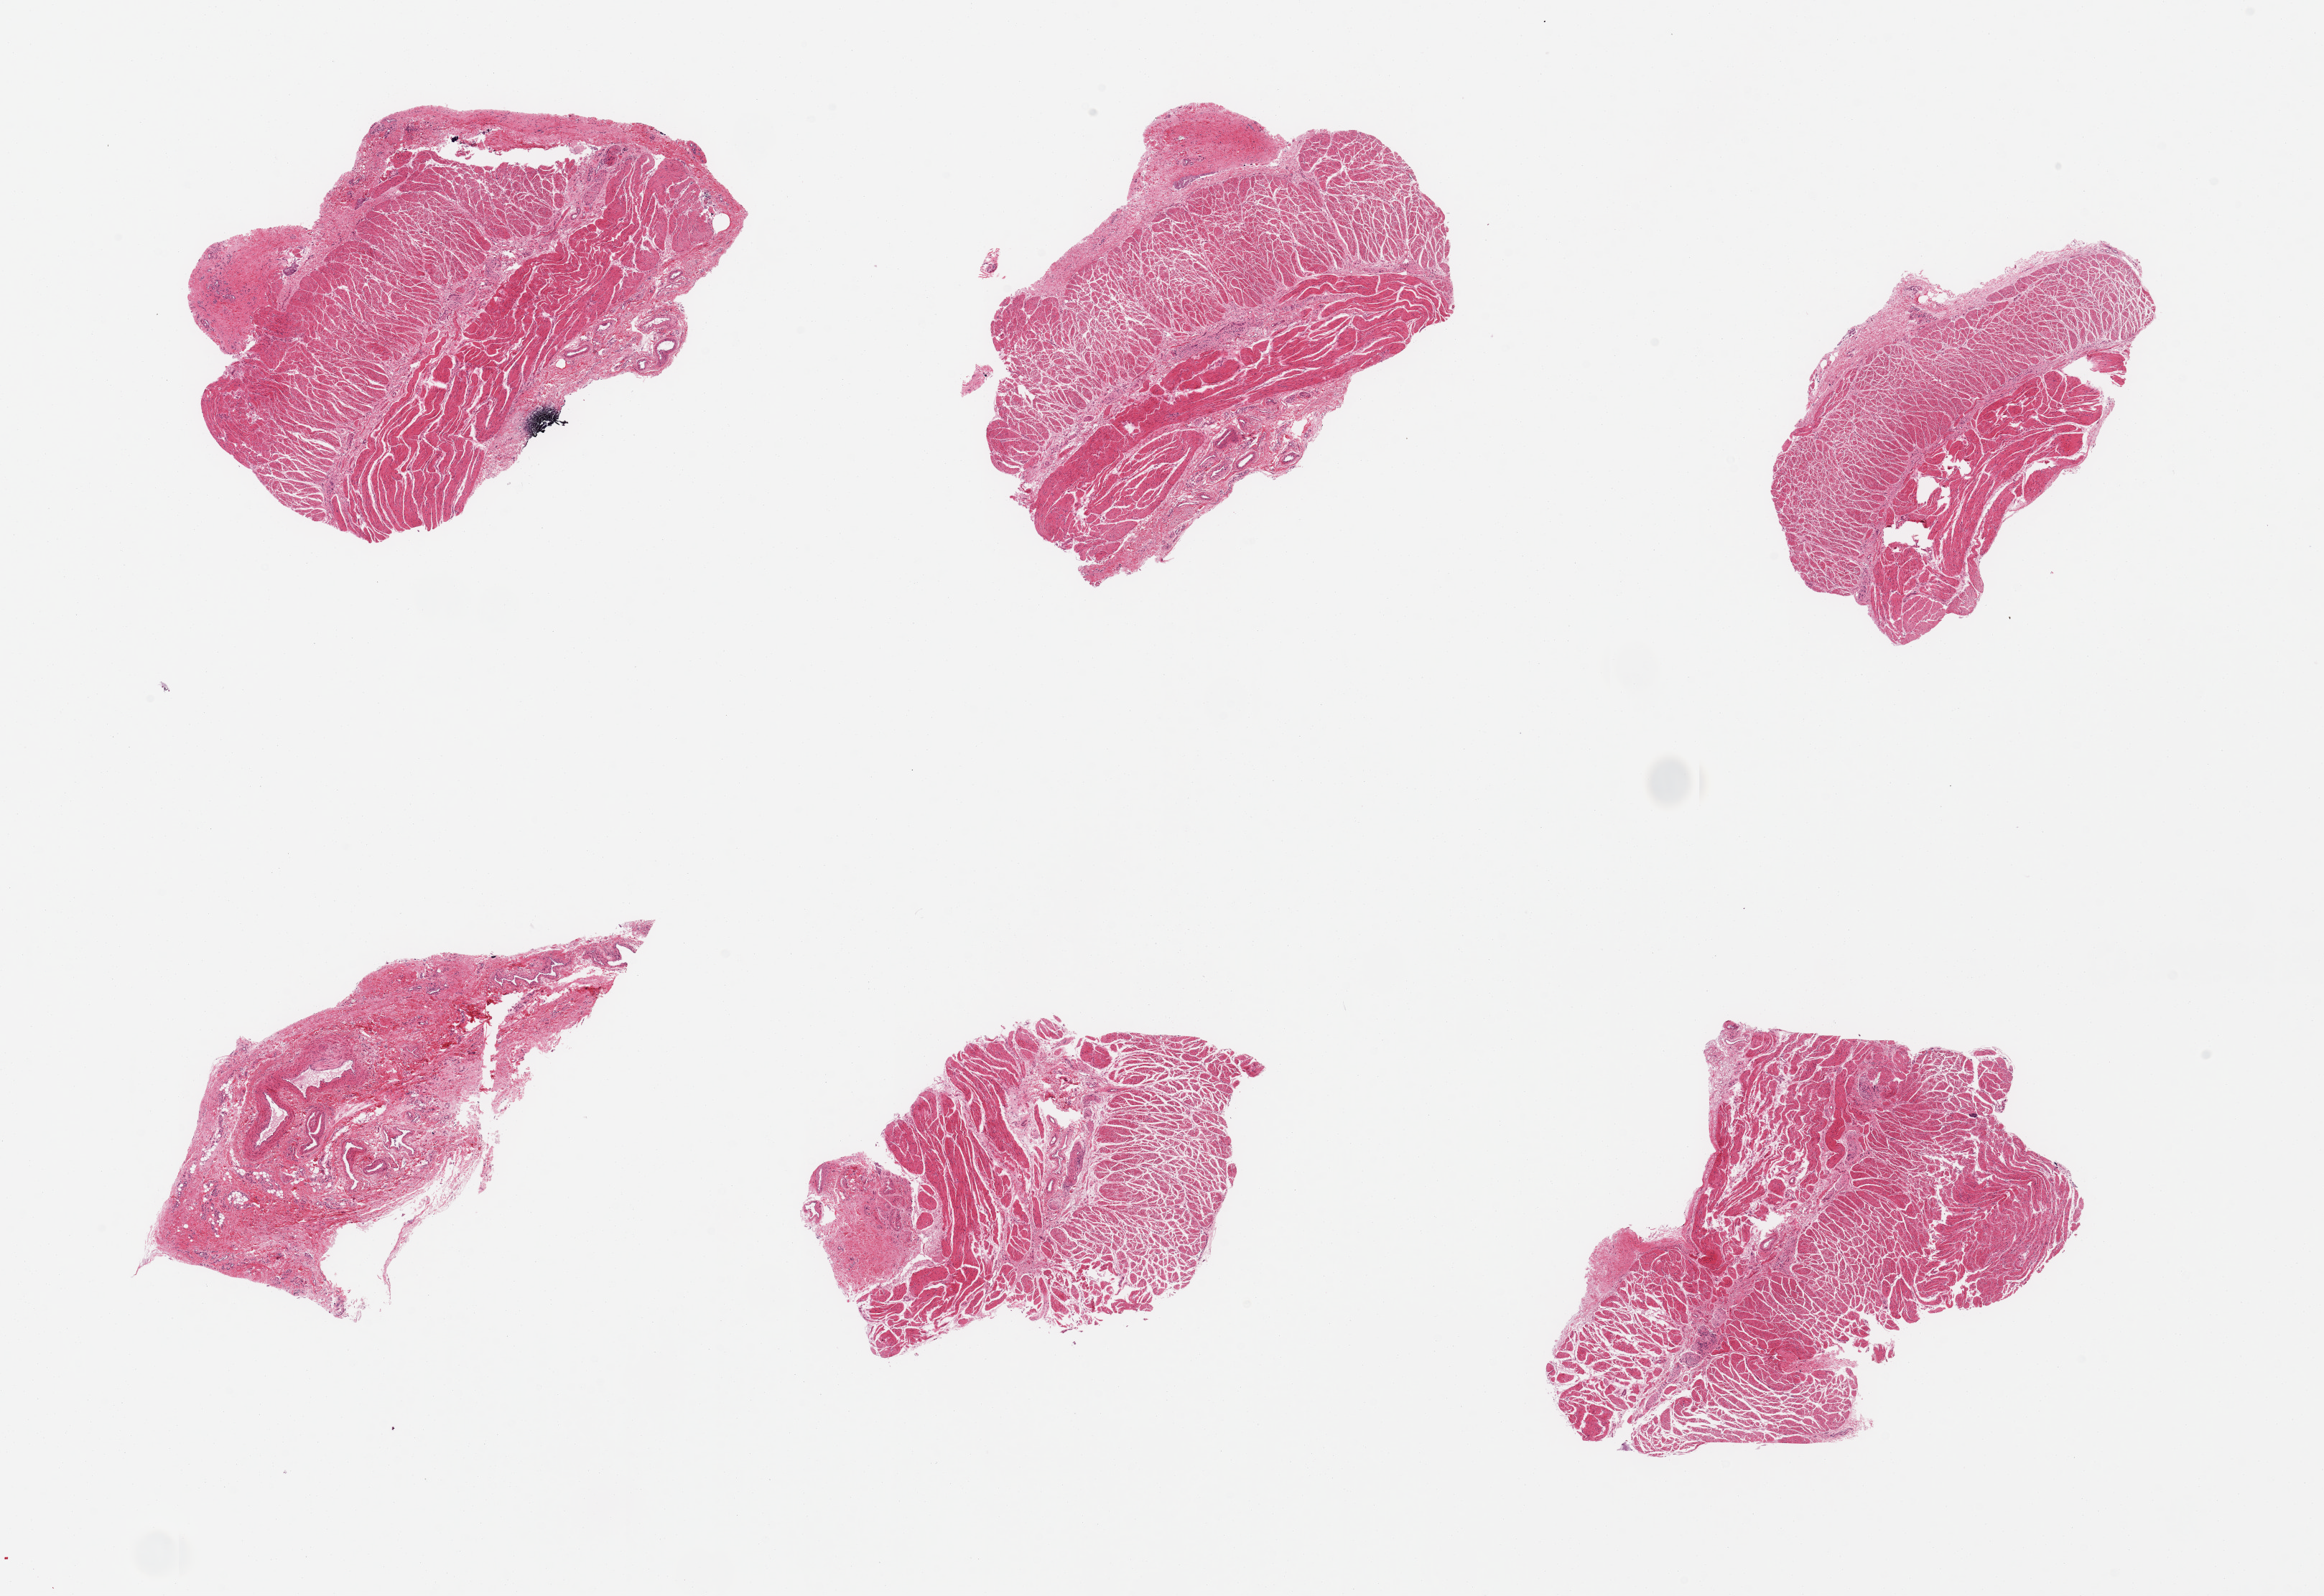
Whole-slide image, haematoxylin and eosin stain, whole scanned area (about 25.6 x 17.6 mm) shown as a low-resolution overview; PAXgene-fixed, paraffin-embedded tissue; sampled site (target tissue): esophageal muscle; tissue donor sample. Donor sex: female.
Pathologist's review note for this sample: 6 pieces, 1 is all fibrovascular tissue; others have up to 10% fibrous content.